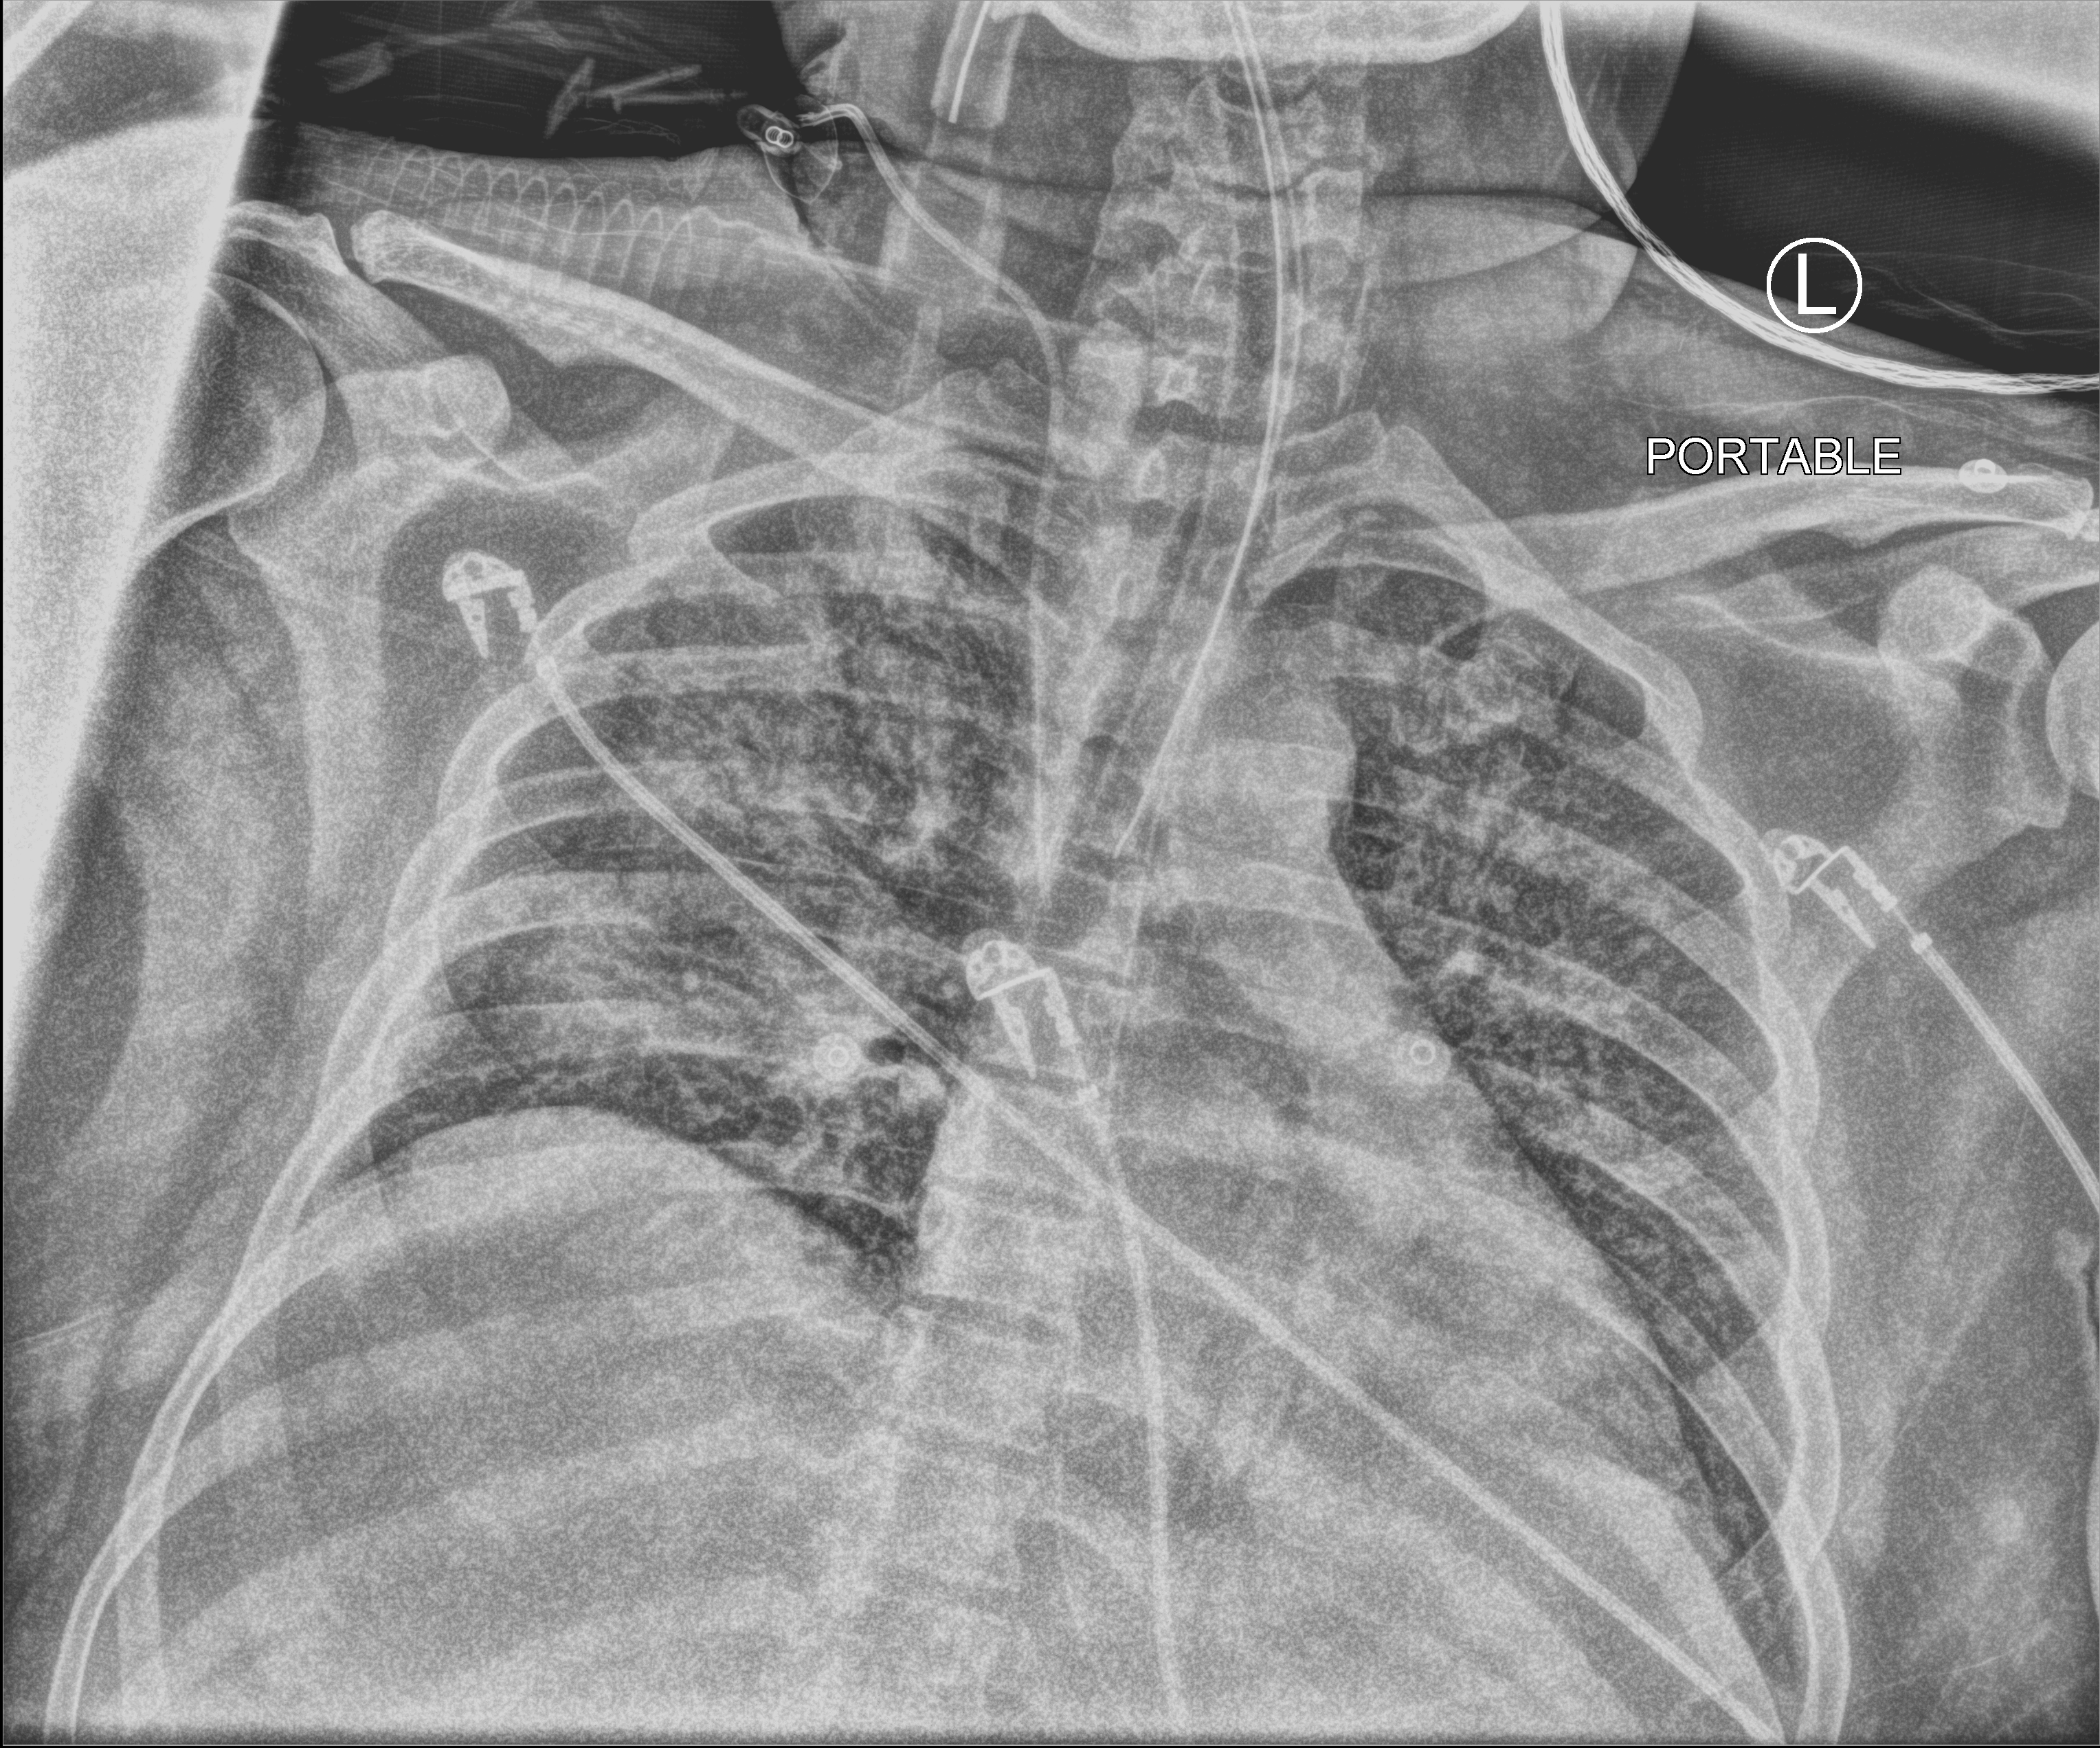
Portable chest radiograph, anteroposterior (AP) projection. Patient hospitalised with COVID-19; male, aged 18–59 years.
Admission-level facts for this patient (not findings on this image; timing relative to this image not recorded): mechanically ventilated during this hospital stay: yes; admitted to intensive care during this hospital stay: yes.